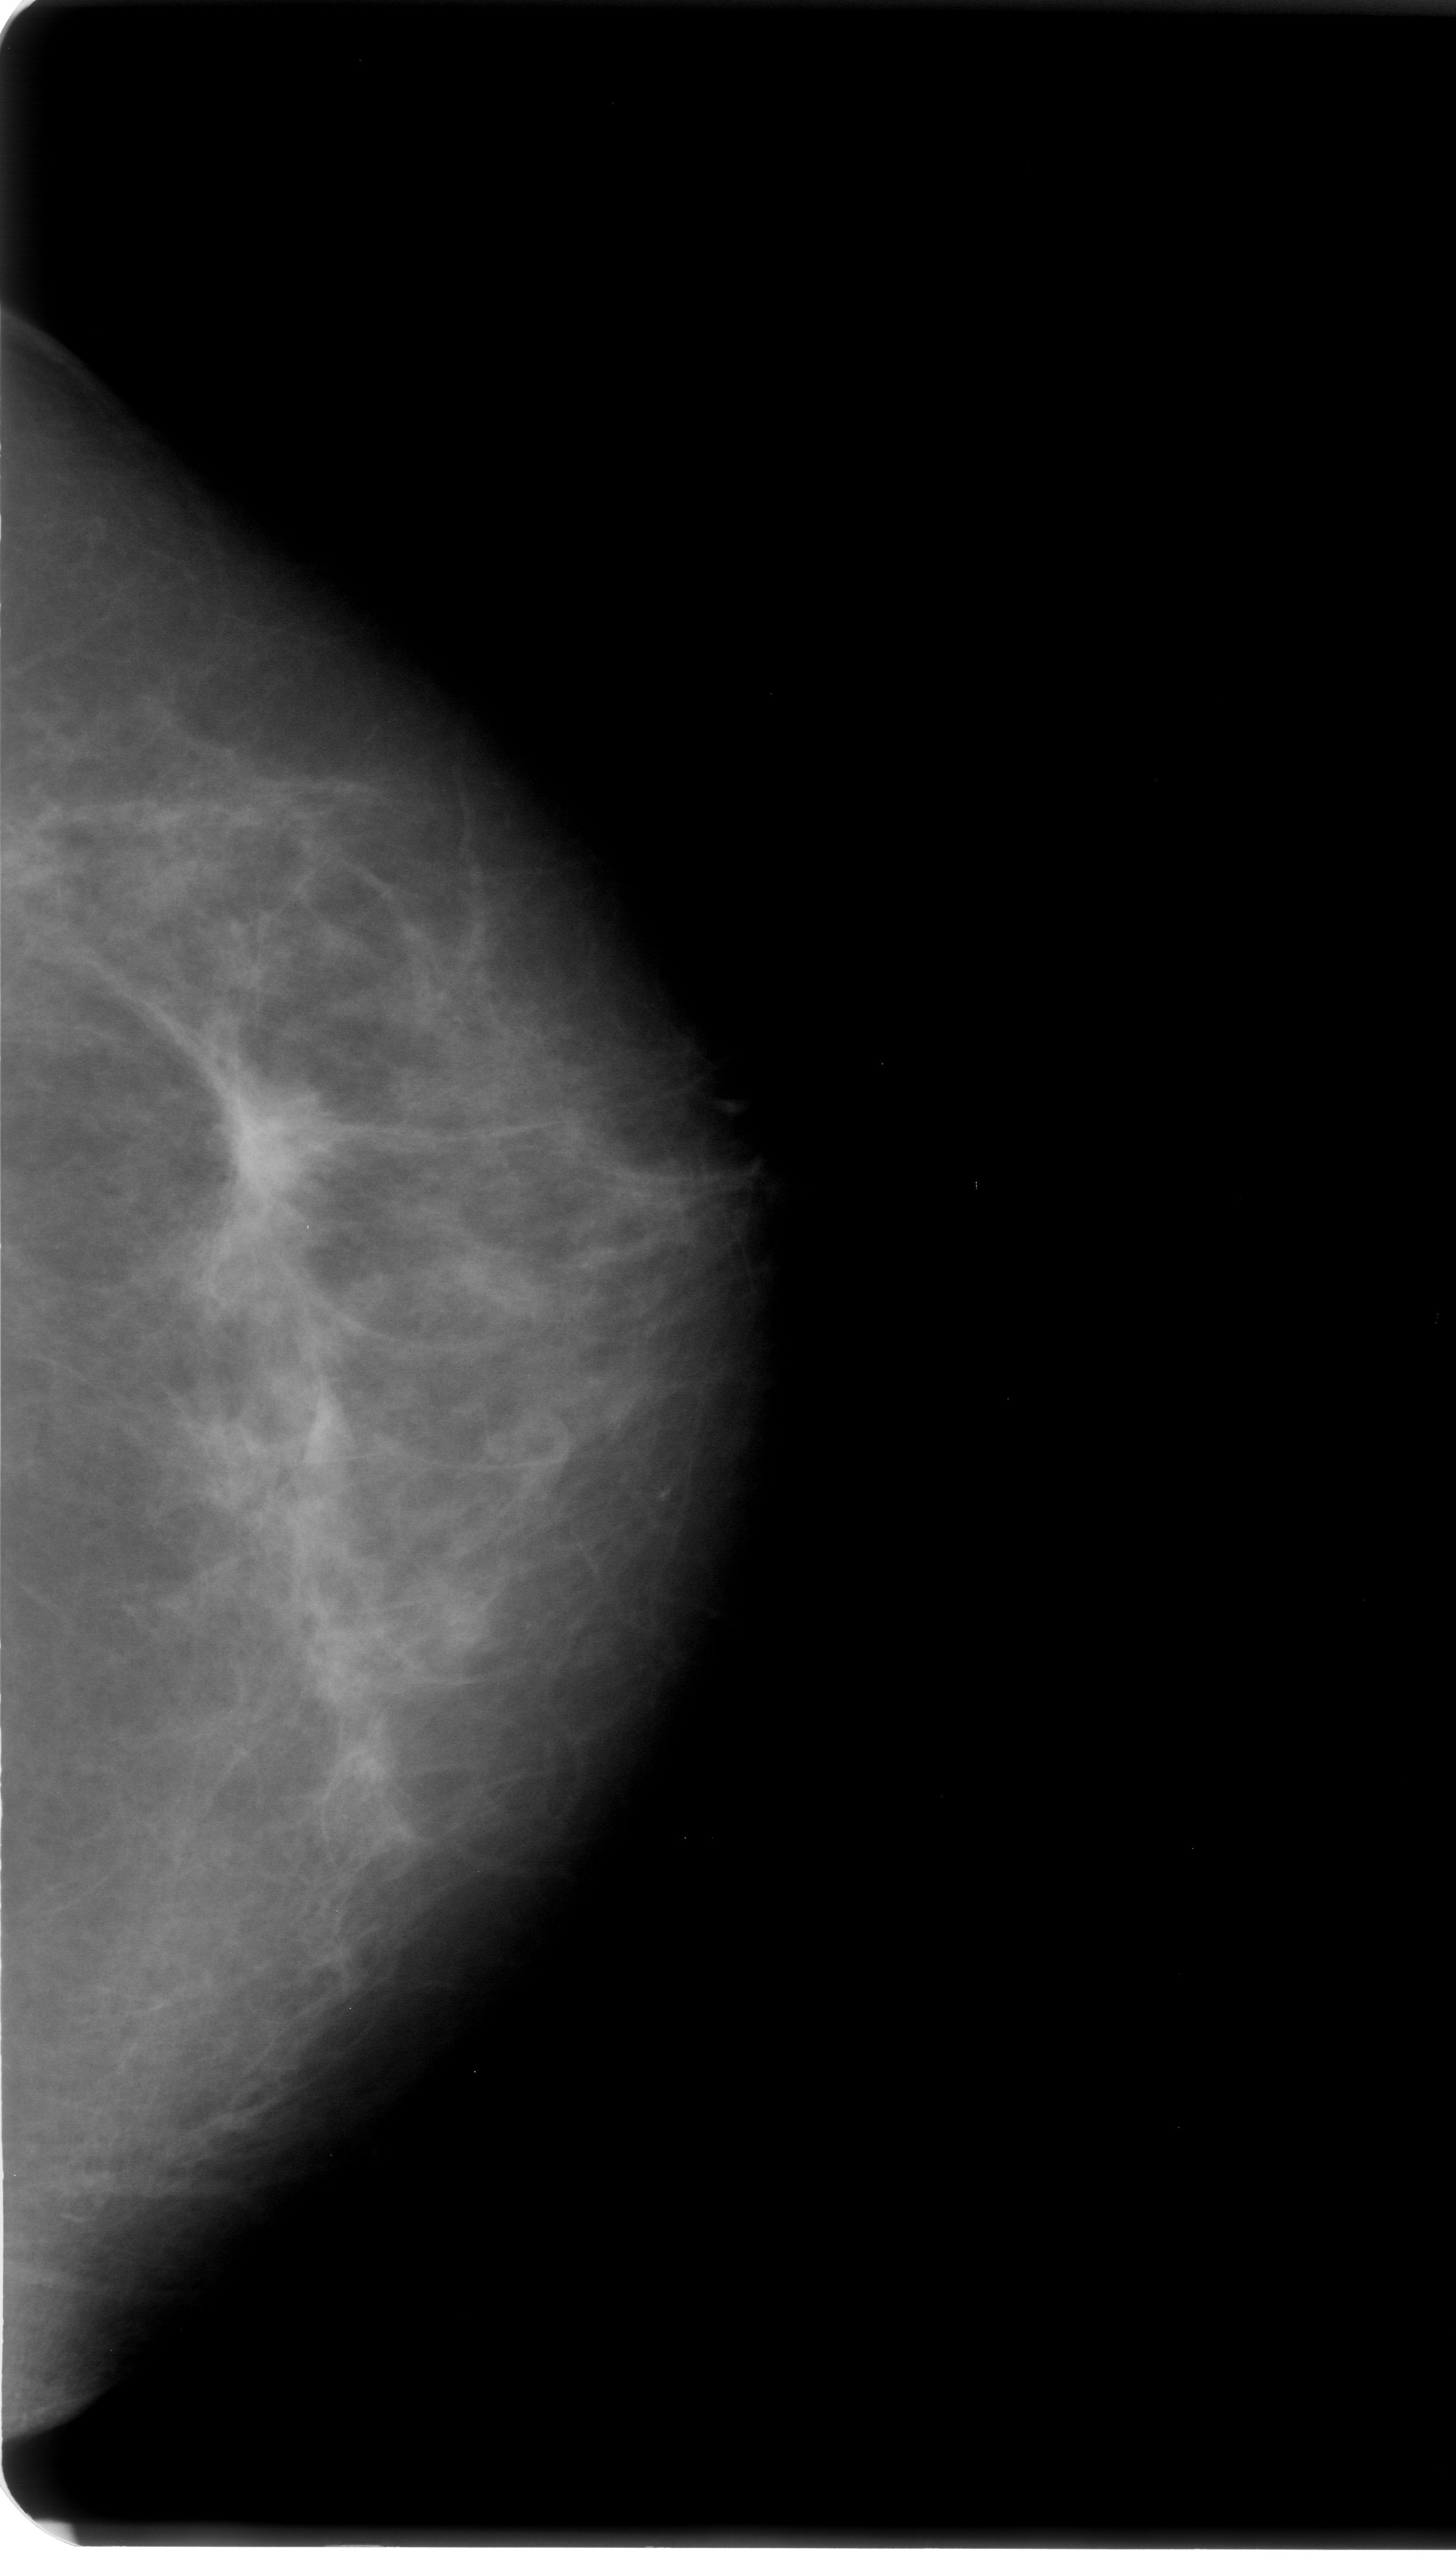
Mammogram (digitized film). Left breast. CC view. 1456 × 2554 image matrix.
Expert-marked regions of interest on this image (one box per marked abnormality):
- mass, shape irregular / architectural distortion, margins spiculated; BI-RADS assessment category 4; subtlety rating 4 on a 1 (subtle) to 5 (obvious) scale; pathology result (as recorded, not read from the image): malignant: bounding box (x1, y1, x2, y2) in pixels: (176, 1064, 320, 1249)